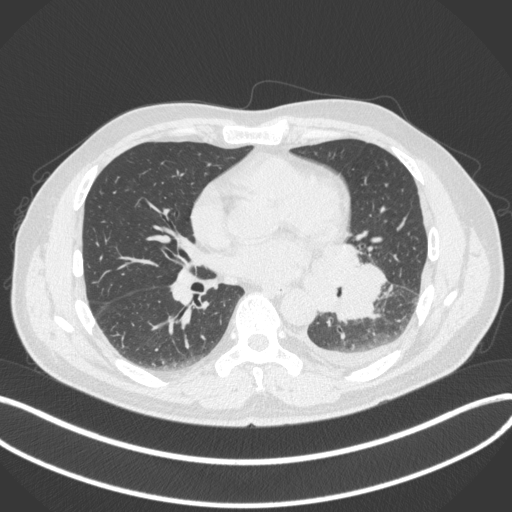
Chest CT, one axial slice; position 171 of 350 along the scan axis; 120 kVp; lung window (W 1500 / L -600 HU); 1 mm slice thickness; 512 × 512 image matrix, field of view 400 × 400 mm. Patient: male, 58 years. Case-level facts recorded for this patient, not image findings: clinical TNM (as recorded): T3 N1 M1b; histopathological grade: G3.
Structures marked on this image (rectangle marked by the reading radiologist):
- lung tumour (recorded histology: small cell carcinoma): bounding box (x1, y1, x2, y2) in pixels: (318, 248, 390, 326)